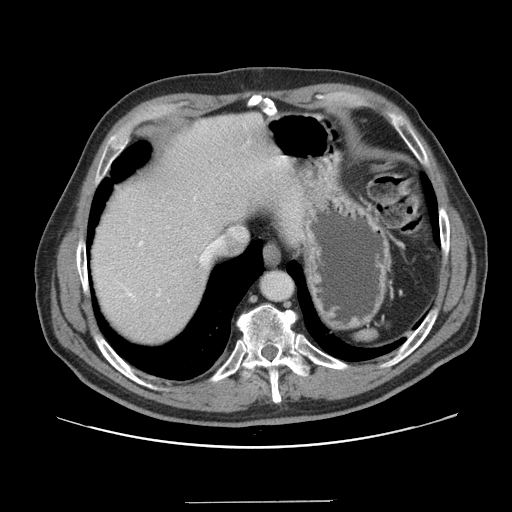
Contrast-enhanced abdominal CT, one axial slice; position 133 of 151 along the scan axis; 120 kVp; intravenous contrast given; soft-tissue window (W 400 / L 40 HU); 512 × 512 image matrix. Male patient, age 63 years. From the clinical record (not read from this slice): diagnosis: colorectal cancer liver metastases, imaged before liver resection; multiple liver metastases: no; largest metastasis: 2.1 cm; disease in both lobes: no.
Outlined on this slice (manually delineated by an expert):
- hepatic veins: box from (x=200, y=239) to (x=221, y=261) px
- liver: (x=91, y=114)–(x=305, y=347)
- planned liver remnant (the part of the liver to remain after resection): (x=91, y=130)–(x=243, y=347)